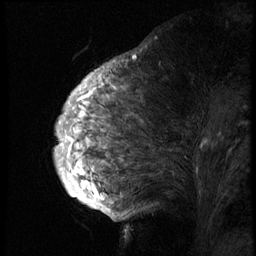
Breast MRI (dynamic contrast-enhanced), one sagittal slice; slice 29 of 74 in the series (ordered by position); 3 images stored at this slice position (order not interpretable as contrast timing); 1.5 T; TE 4.2 ms, TR 8.9 ms; 256 × 256 image matrix, field of view 200 × 200 mm. Female patient, age 57 years. From the clinical record (not read from this slice): setting: breast cancer imaged before/during neoadjuvant chemotherapy; receptor status: HER2-positive.
Annotated regions visible in this slice (semi-automatically segmented with operator editing):
- analysis volume of interest (the breast-tissue region the enhancement analysis was run in; not a lesion): bounding box [x1, y1, x2, y2] px = [53, 67, 249, 173]
- tumour enhancement mask (voxels above the 140 % enhancement threshold inside the analysis volume of interest): [88, 96, 90, 98]